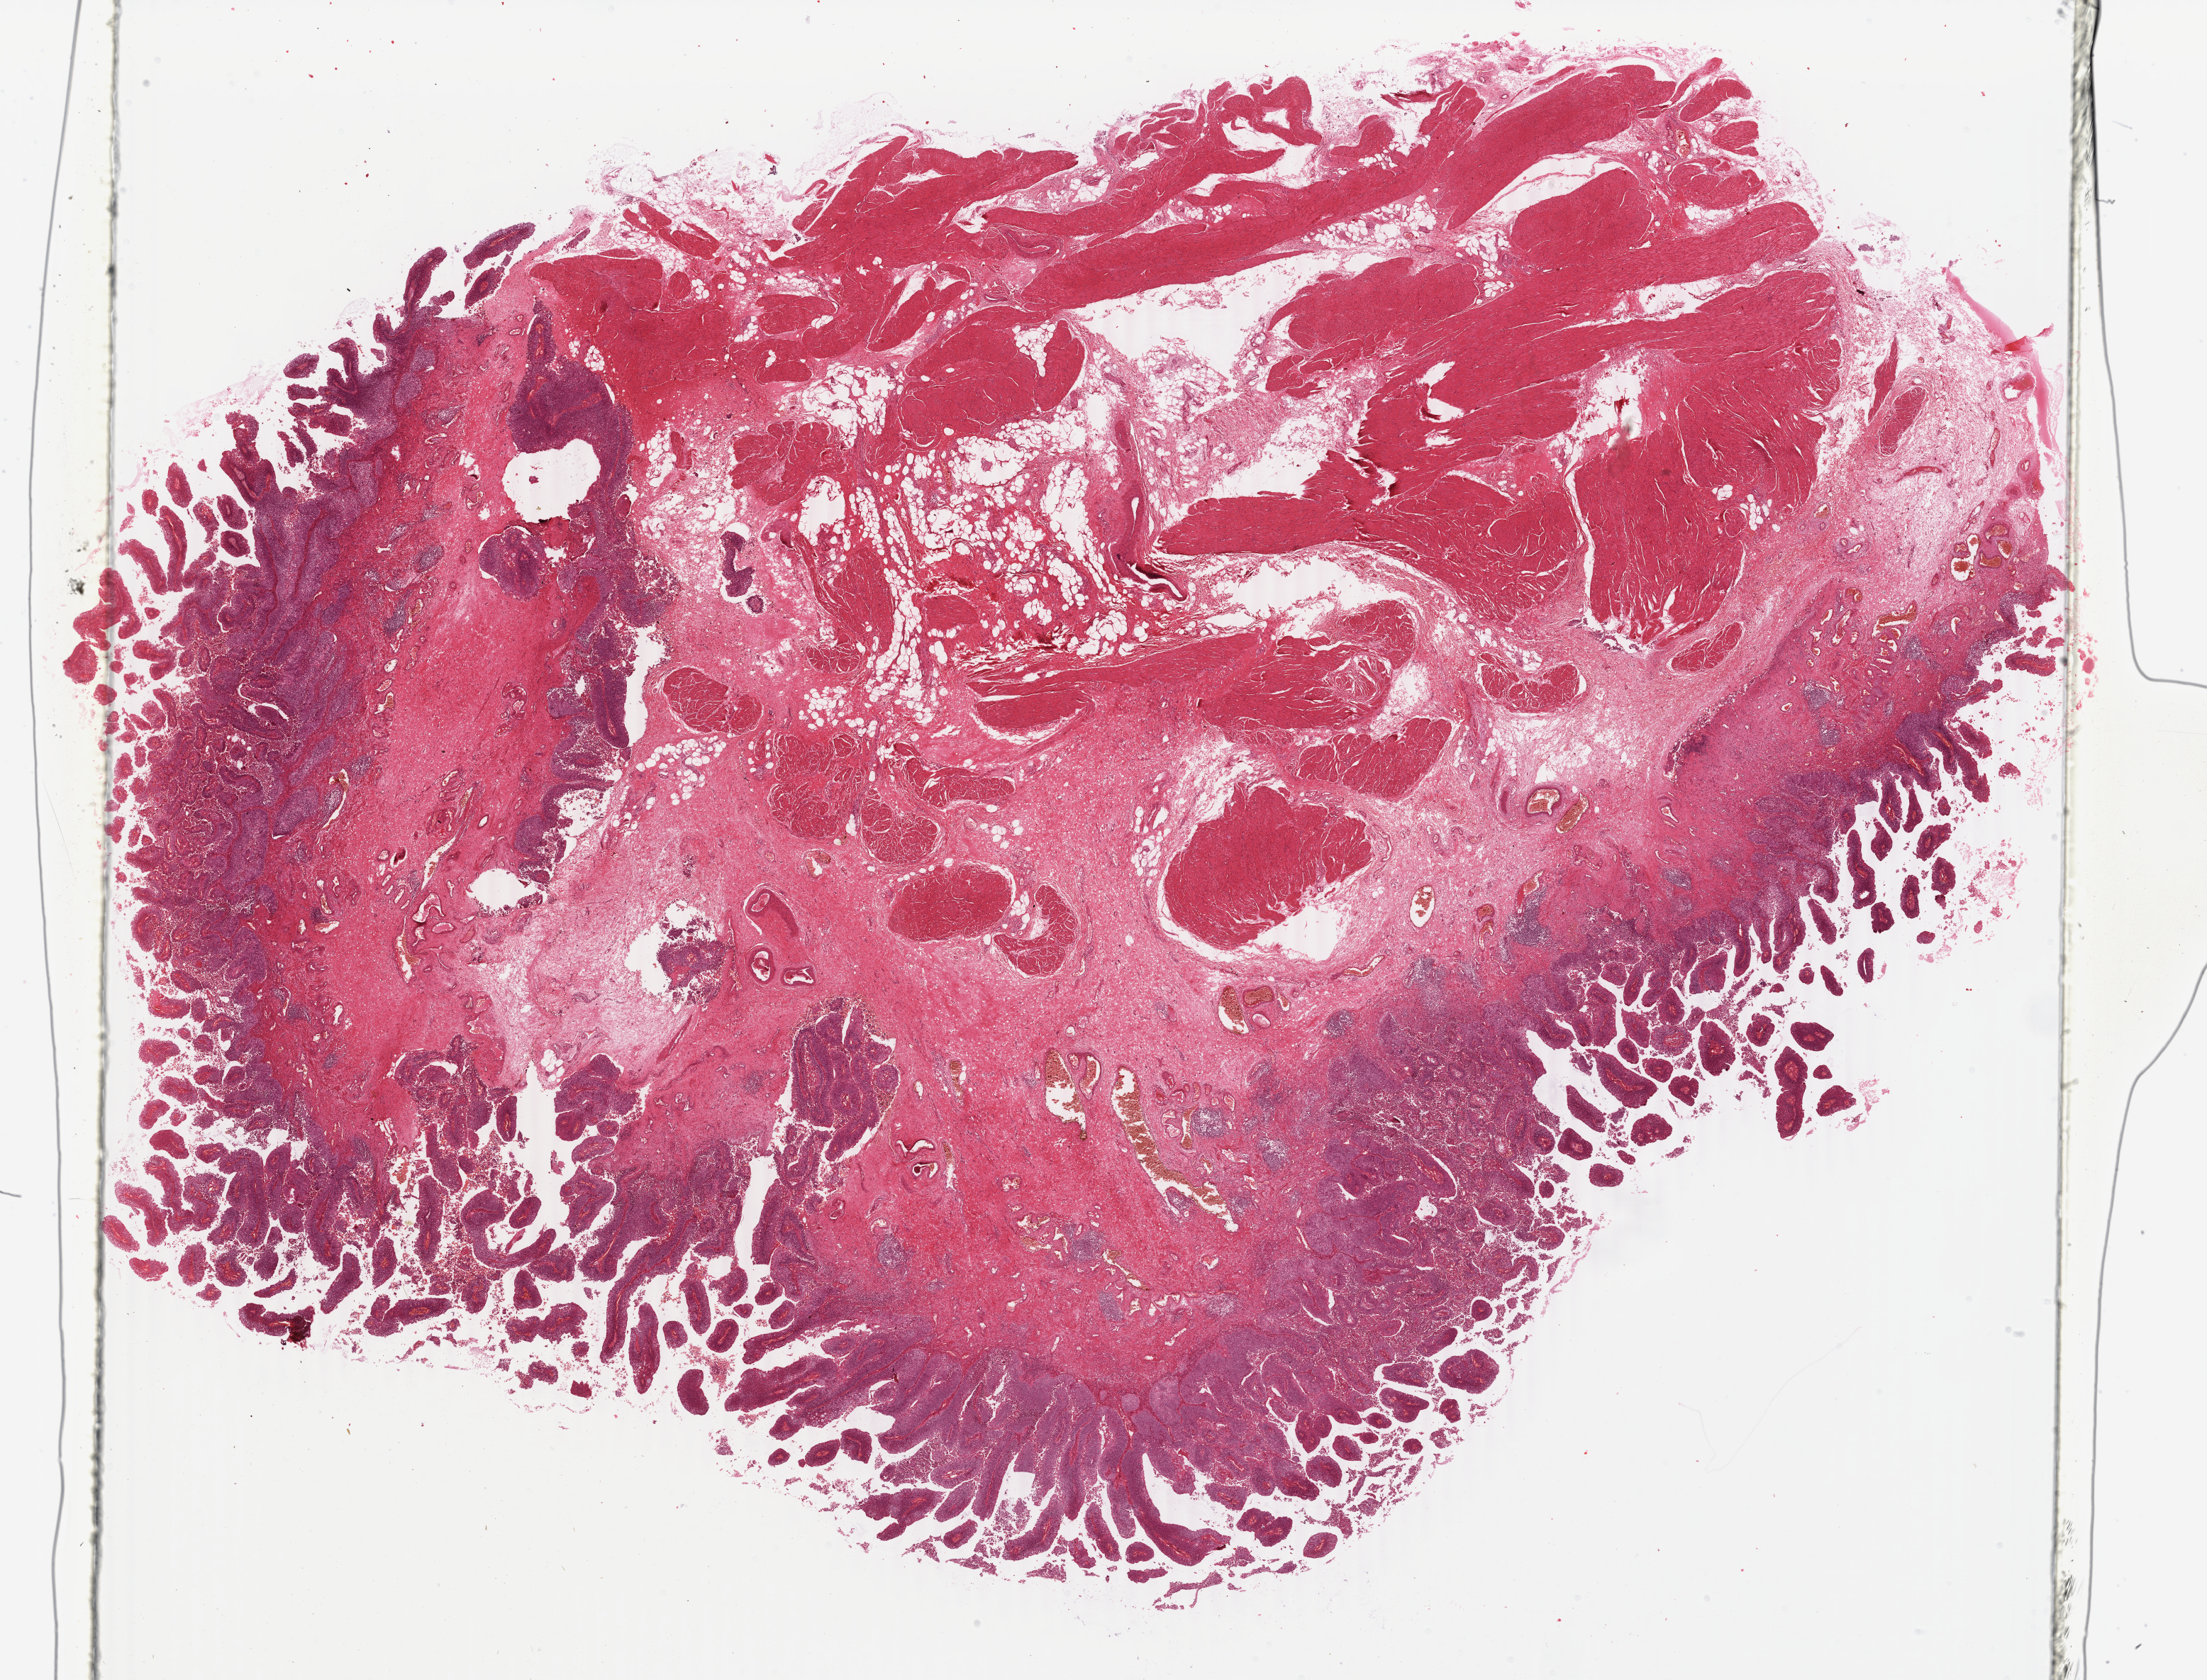
Whole-slide histology image, H&E-stained, shown as a low-resolution overview of the whole scanned area (about 24.7 x 18.8 mm). FFPE section. Bladder, primary tumour sample. Male patient; age at initial diagnosis 60 years. Histologic grade: low grade.
* AJCC pathologic stage: II (7th edition)
* TNM: T2 N0 M0
* diagnosis: Papillary transitional cell carcinoma